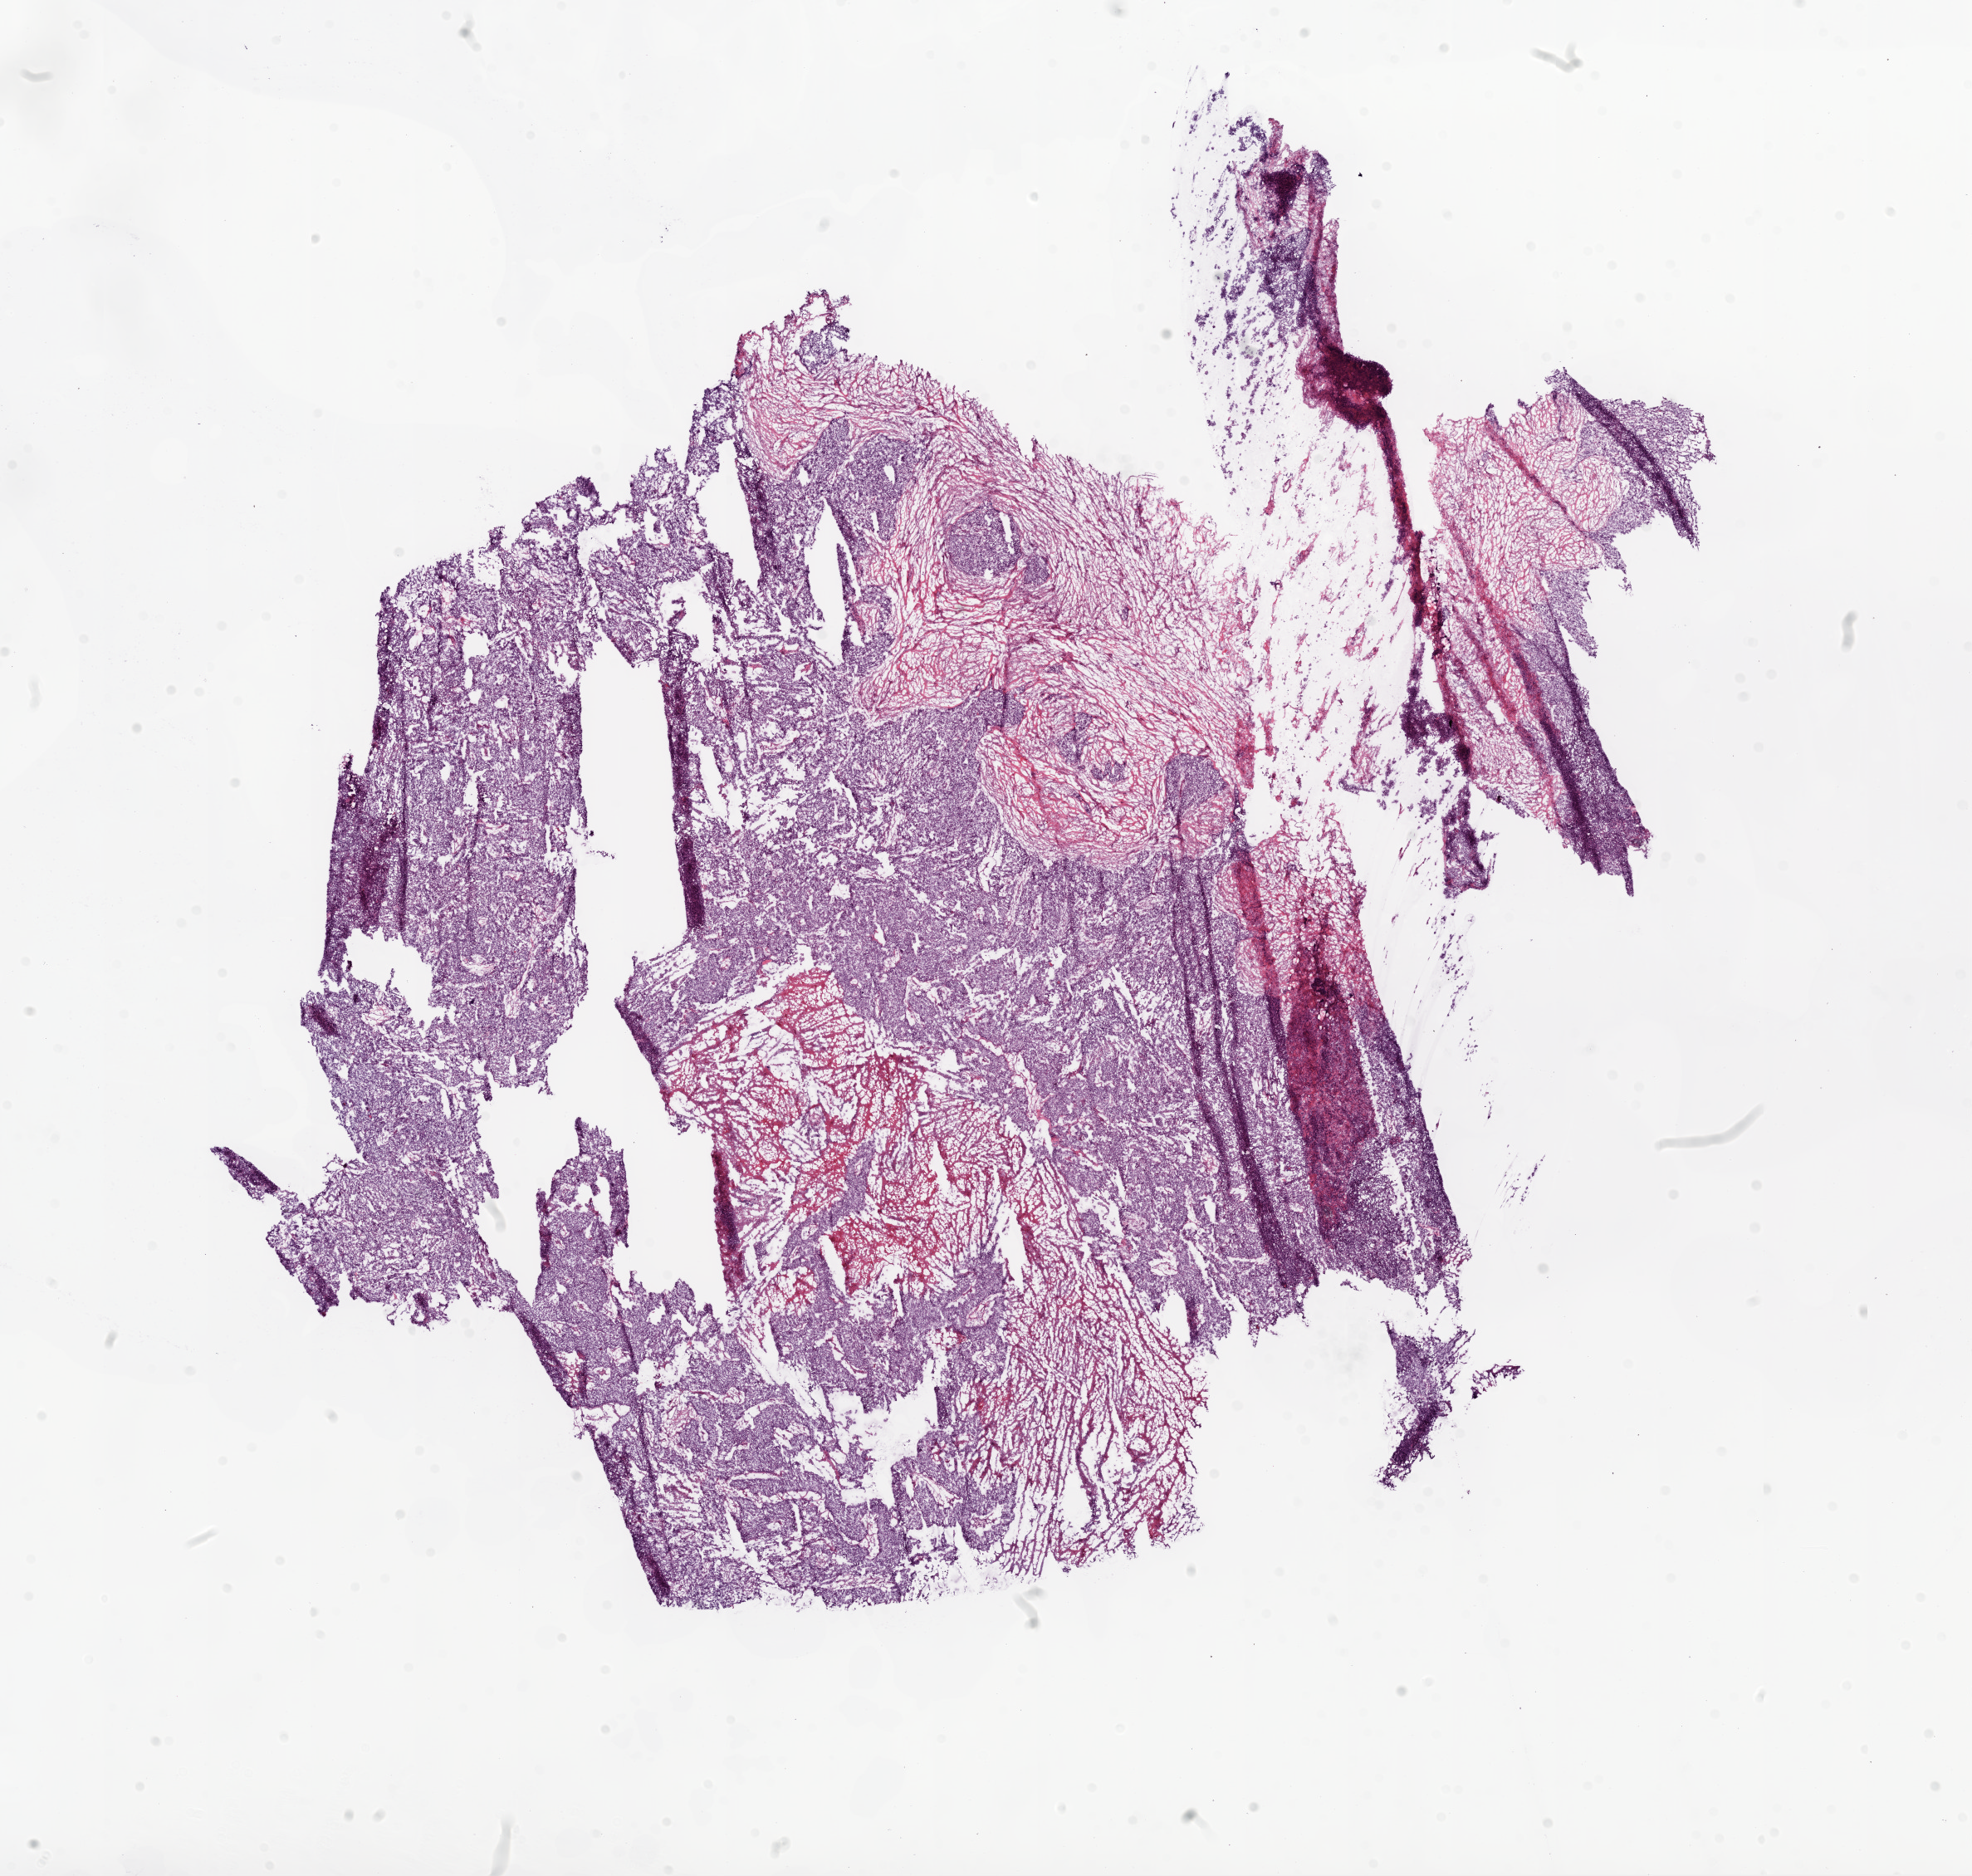
Digitized H&E tissue section (whole slide) — low-resolution overview of the scanned area, about 19.1 x 18.1 mm; frozen section from the top of the tissue portion; sample: primary tumour, ovary. Patient: female, age at initial diagnosis 56 years. Slide review estimates, as recorded: tumour cells 70%, tumour nuclei 85%.
Histologic diagnosis: Serous cystadenocarcinoma, NOS (specified parts of peritoneum).